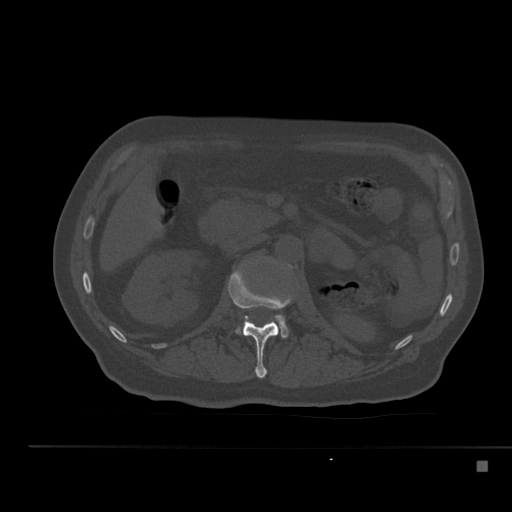
CT including the spine, one axial slice. Slice 202 of 517 in the series (ordered by position). Reconstruction kernel Br40s. Bone window (W 1800 / L 400 HU). 1.5 mm slice thickness. 512 × 512 image matrix. Patient: male, 70 years. From the clinical record (not read from this slice): primary cancer: renal; vertebrae with lytic lesions (as recorded): T4, T6, T10, T12, L3, L4, L5.
Structures marked on this image (semi-automatically segmented with operator editing):
- L1 vertebra: box from (x=228, y=268) to (x=293, y=378) px
- L2 vertebra: (x=236, y=315)–(x=288, y=338)